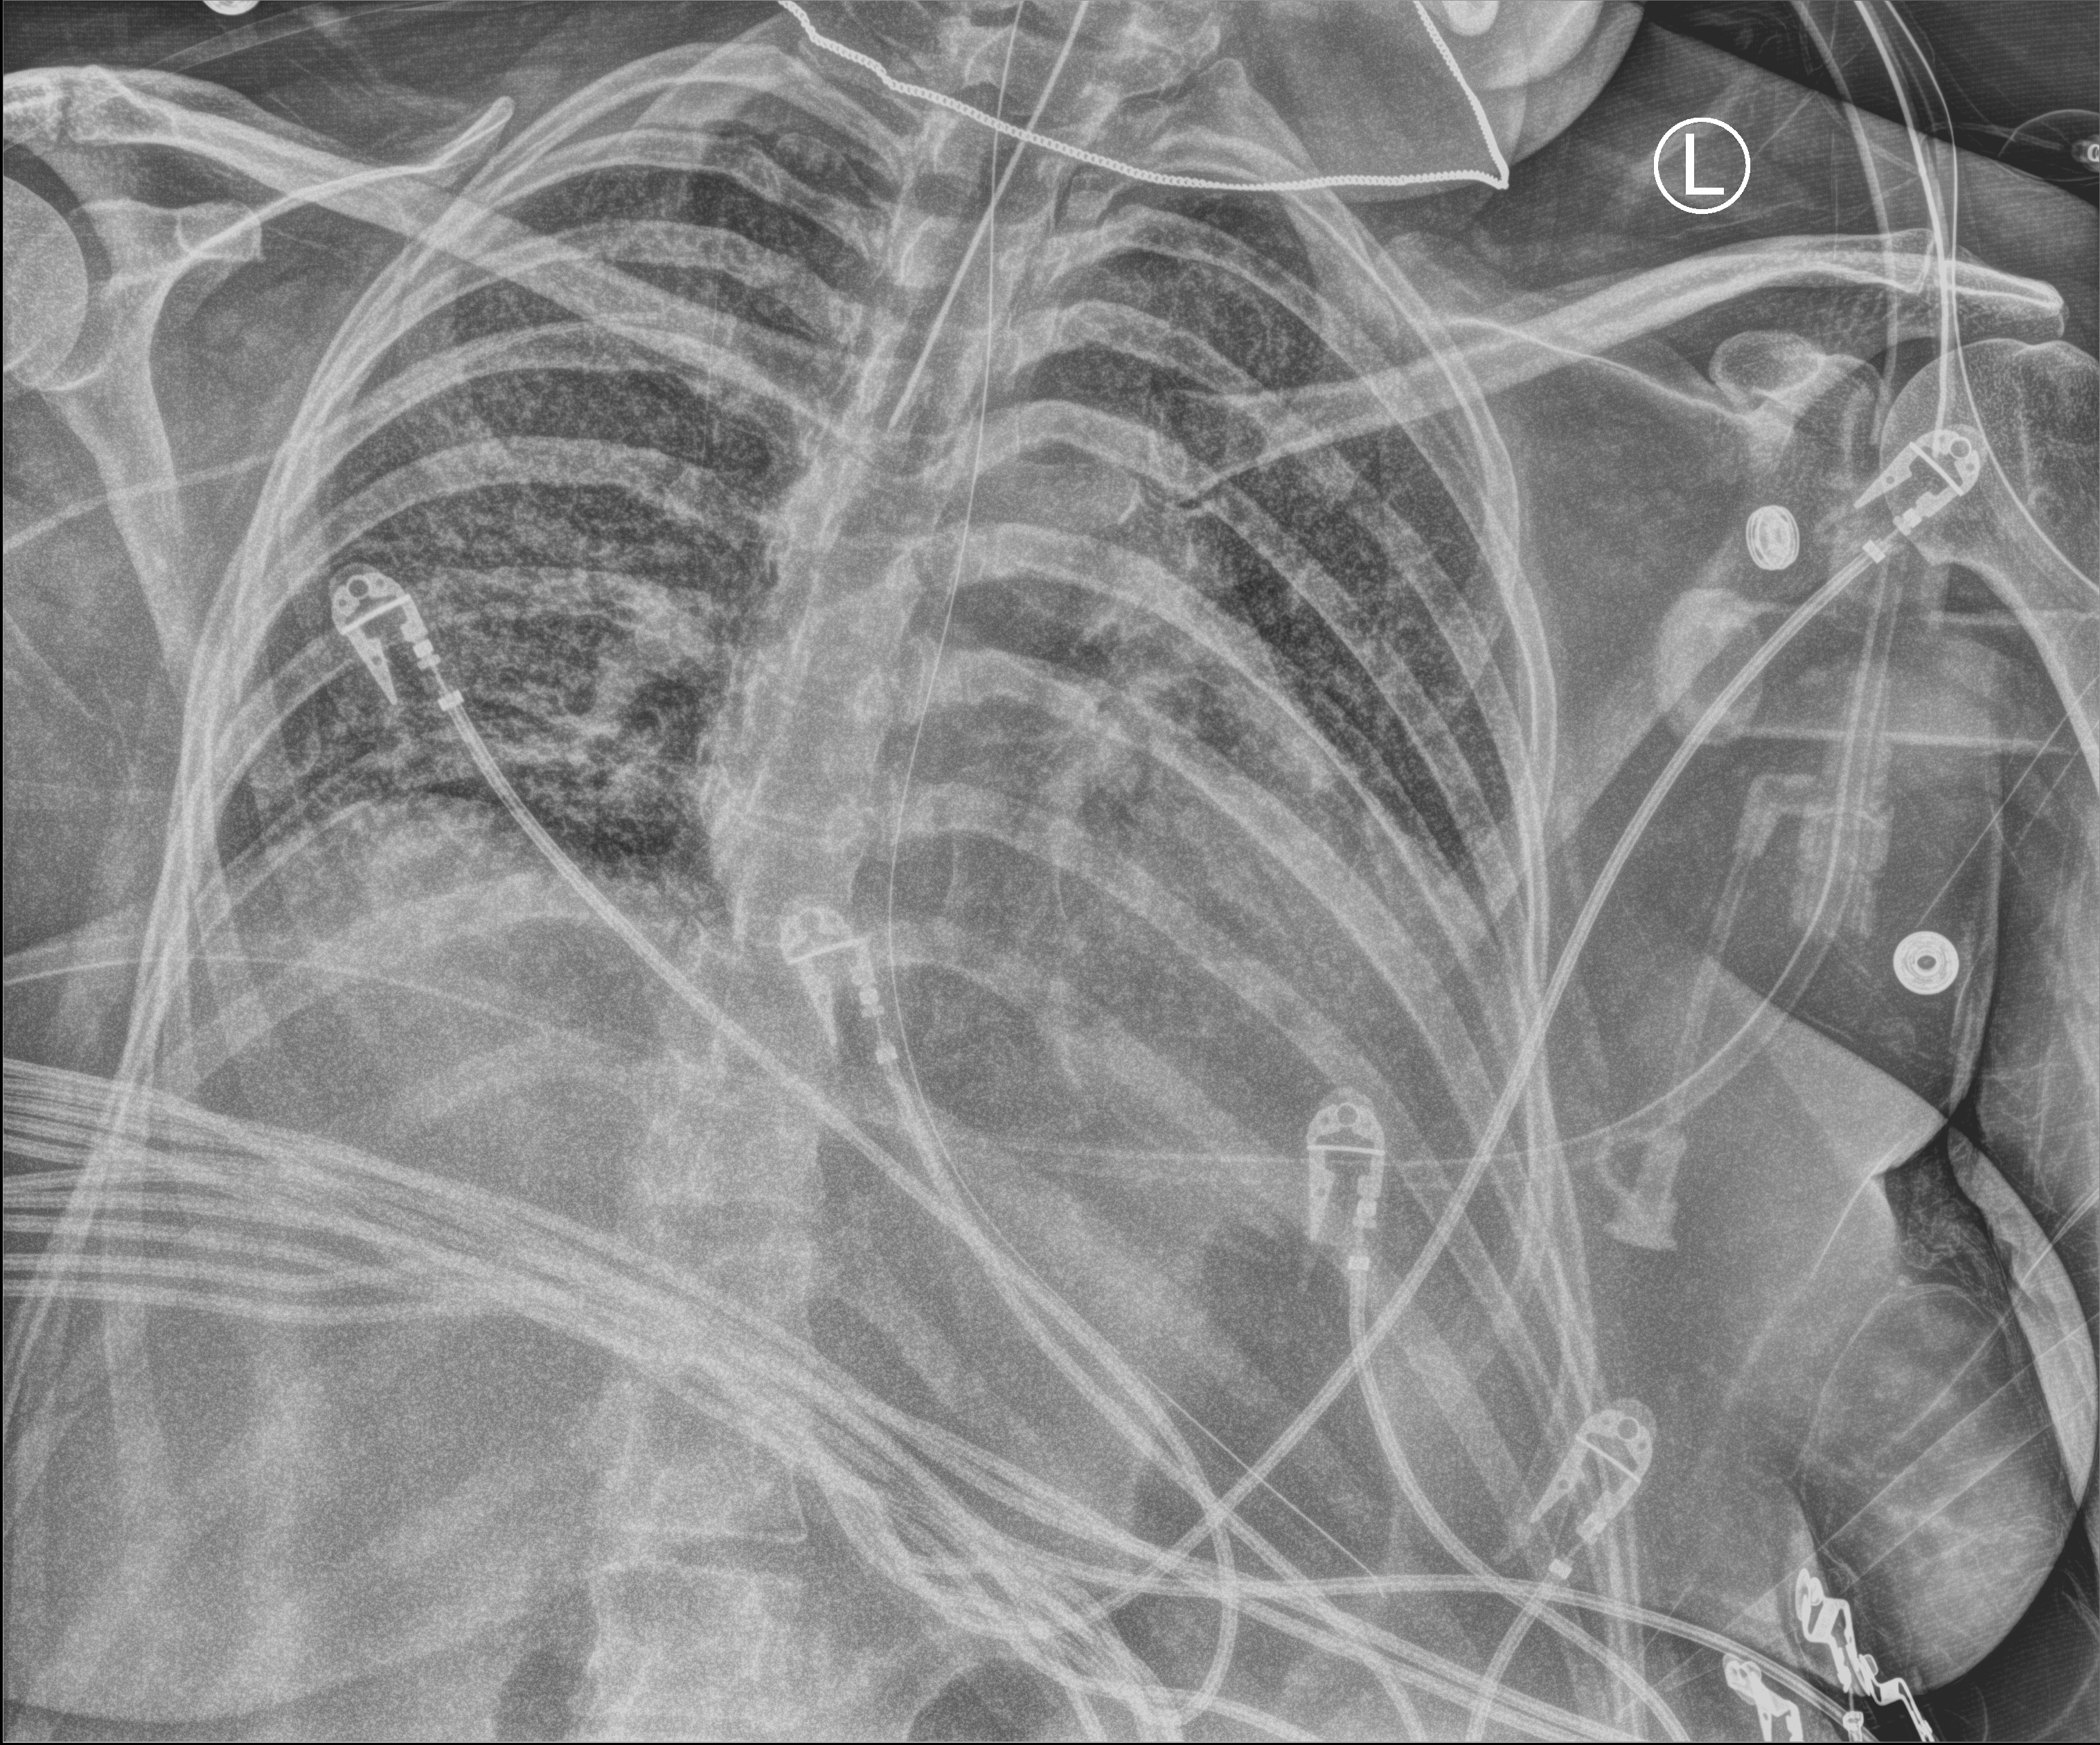
Bedside chest radiograph (computed radiography); anteroposterior (AP) projection. Female patient hospitalised with COVID-19, age 18–59 years.
Hospital-stay facts (about this admission, not read from this image; timing relative to this image not recorded): mechanically ventilated during this hospital stay: yes; admitted to intensive care during this hospital stay: yes.